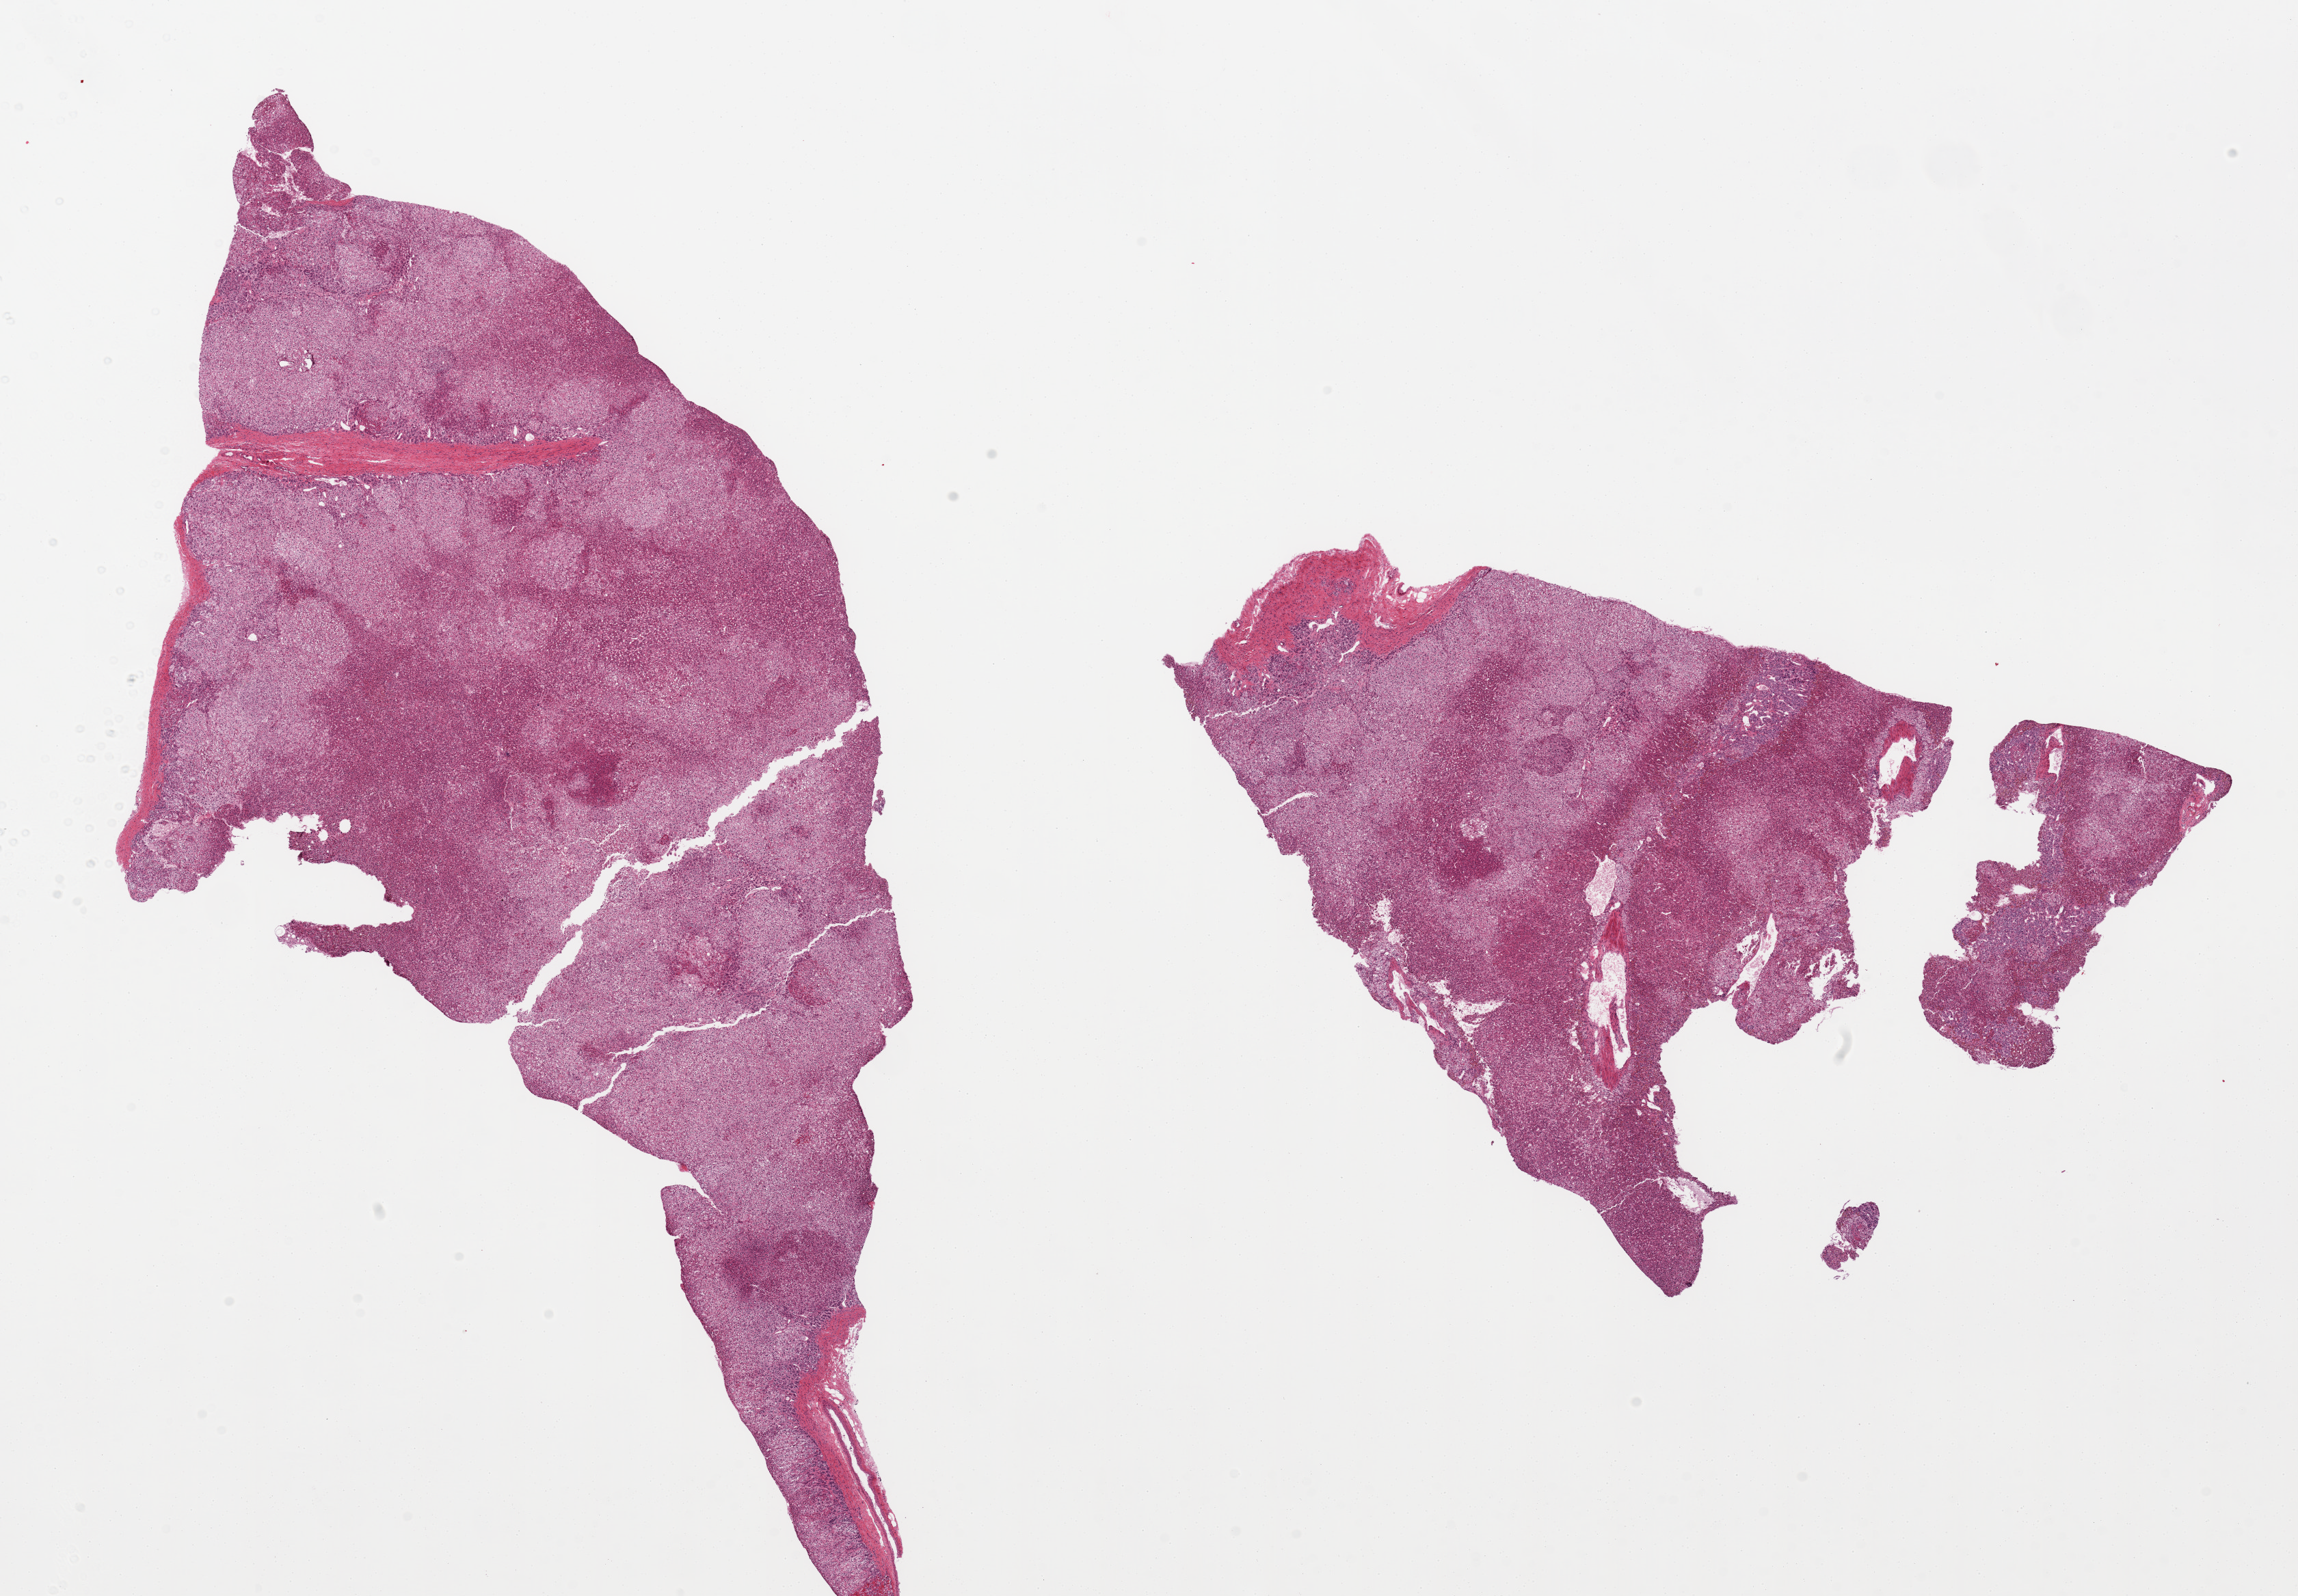
Whole-slide image, haematoxylin and eosin stain, brightfield, shown as a low-resolution overview of the whole scanned area (about 26.6 x 18.5 mm, from a 20x scan). PAXgene-fixed, paraffin-embedded tissue. Sampled site (target tissue): adrenal gland. Tissue donor sample. Donor sex: male.
Pathologist's review note for this sample: 2 pieces.